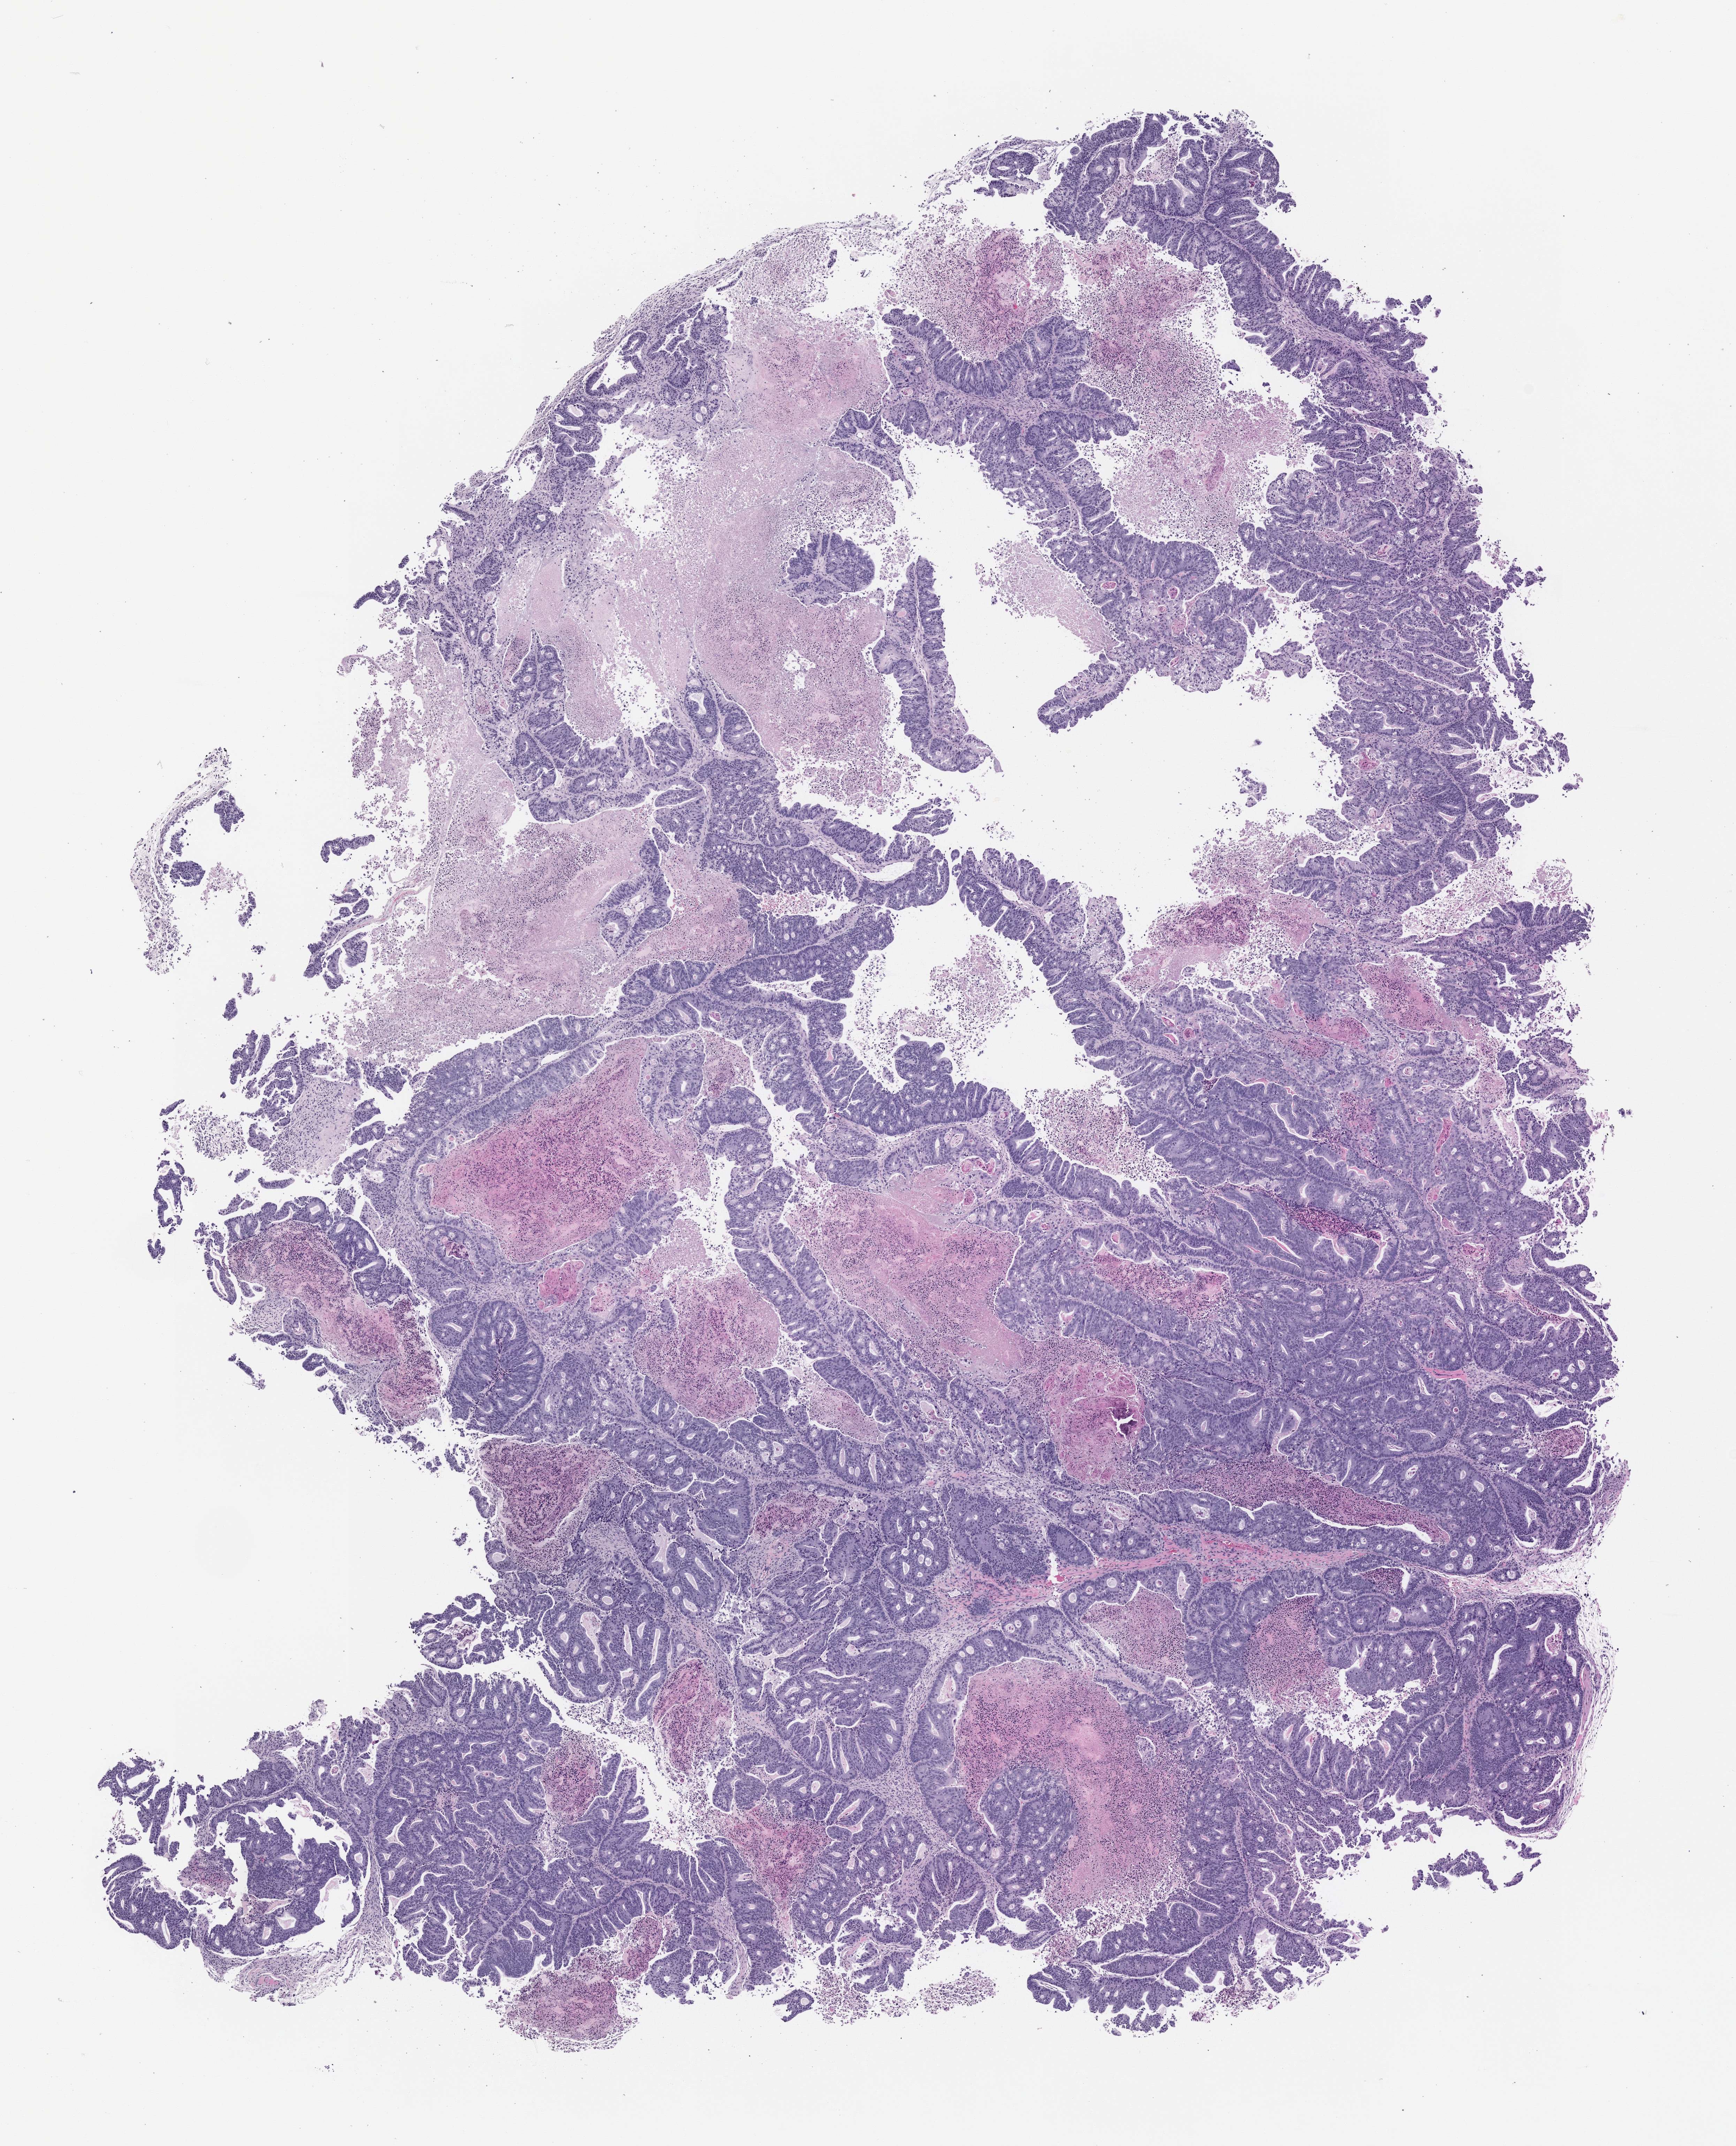
Whole-slide image, haematoxylin and eosin: patient-derived xenograft (human tumor grown in a mouse), passage 2 — a low-resolution overview of the entire scanned area, about 10.0 x 12.4 mm; formalin-fixed paraffin-embedded section; originating tumor site category: colon.
• originating patient diagnosis: Colon Adenocarcinoma